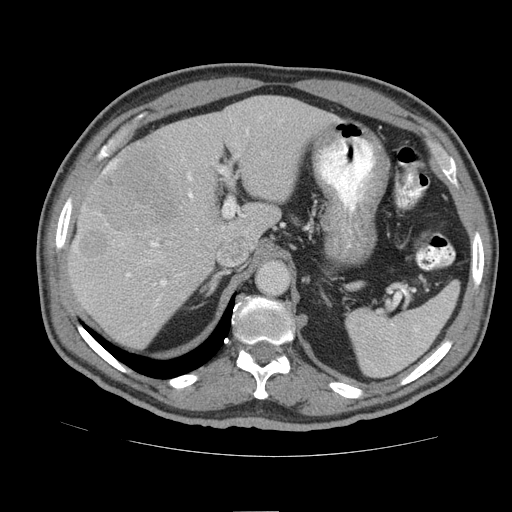
Contrast-enhanced abdominal CT (liver protocol), one axial slice; slice 60 of 105 in the series (ordered by position); reconstruction kernel STANDARD; soft-tissue window (W 400 / L 40 HU); 2.5 mm slice thickness; 512 × 512 image matrix, field of view 380 × 380 mm. Case-level facts recorded for this patient, not image findings: diagnosis: hepatocellular carcinoma (patient treated with transarterial chemoembolisation; whether this scan precedes or follows treatment is not stated here); TNM stage (as recorded): Stage-IIIB; Child-Pugh class: A; tumour nodularity: multinodular.
Outlined on this slice (semi-automatic segmentation, software-assisted and operator-edited):
- liver parenchyma outside the tumour (the mass and vessels are separate outlines, so this box may not span the whole liver): bounding box <68,96,338,348> (left, top, right, bottom; pixels)
- mass: <79,147,177,259>
- liver vessels: <74,130,248,302>